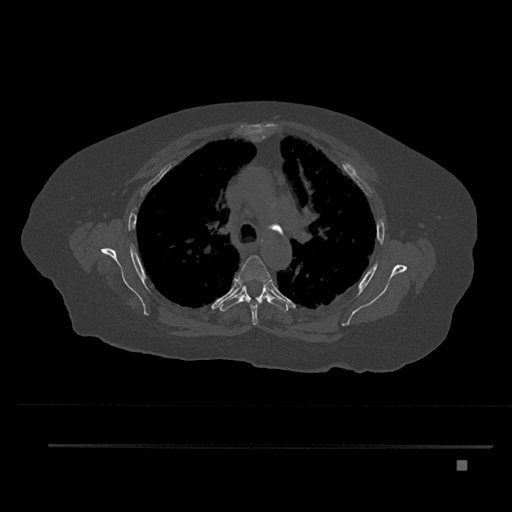
CT including the spine, one axial slice; slice 584 of 797 in the series (ordered by position); bone window (W 1800 / L 400 HU); 512 × 512 image matrix, field of view 437 × 437 mm. Patient: female, 76 years. Case-level facts recorded for this patient, not image findings: primary cancer: lung.
Structures marked on this image (semi-automatic segmentation, software-assisted and operator-edited):
- T4 vertebra: box from (x=236, y=255) to (x=271, y=325) px
- T5 vertebra: (x=220, y=281)–(x=288, y=312)